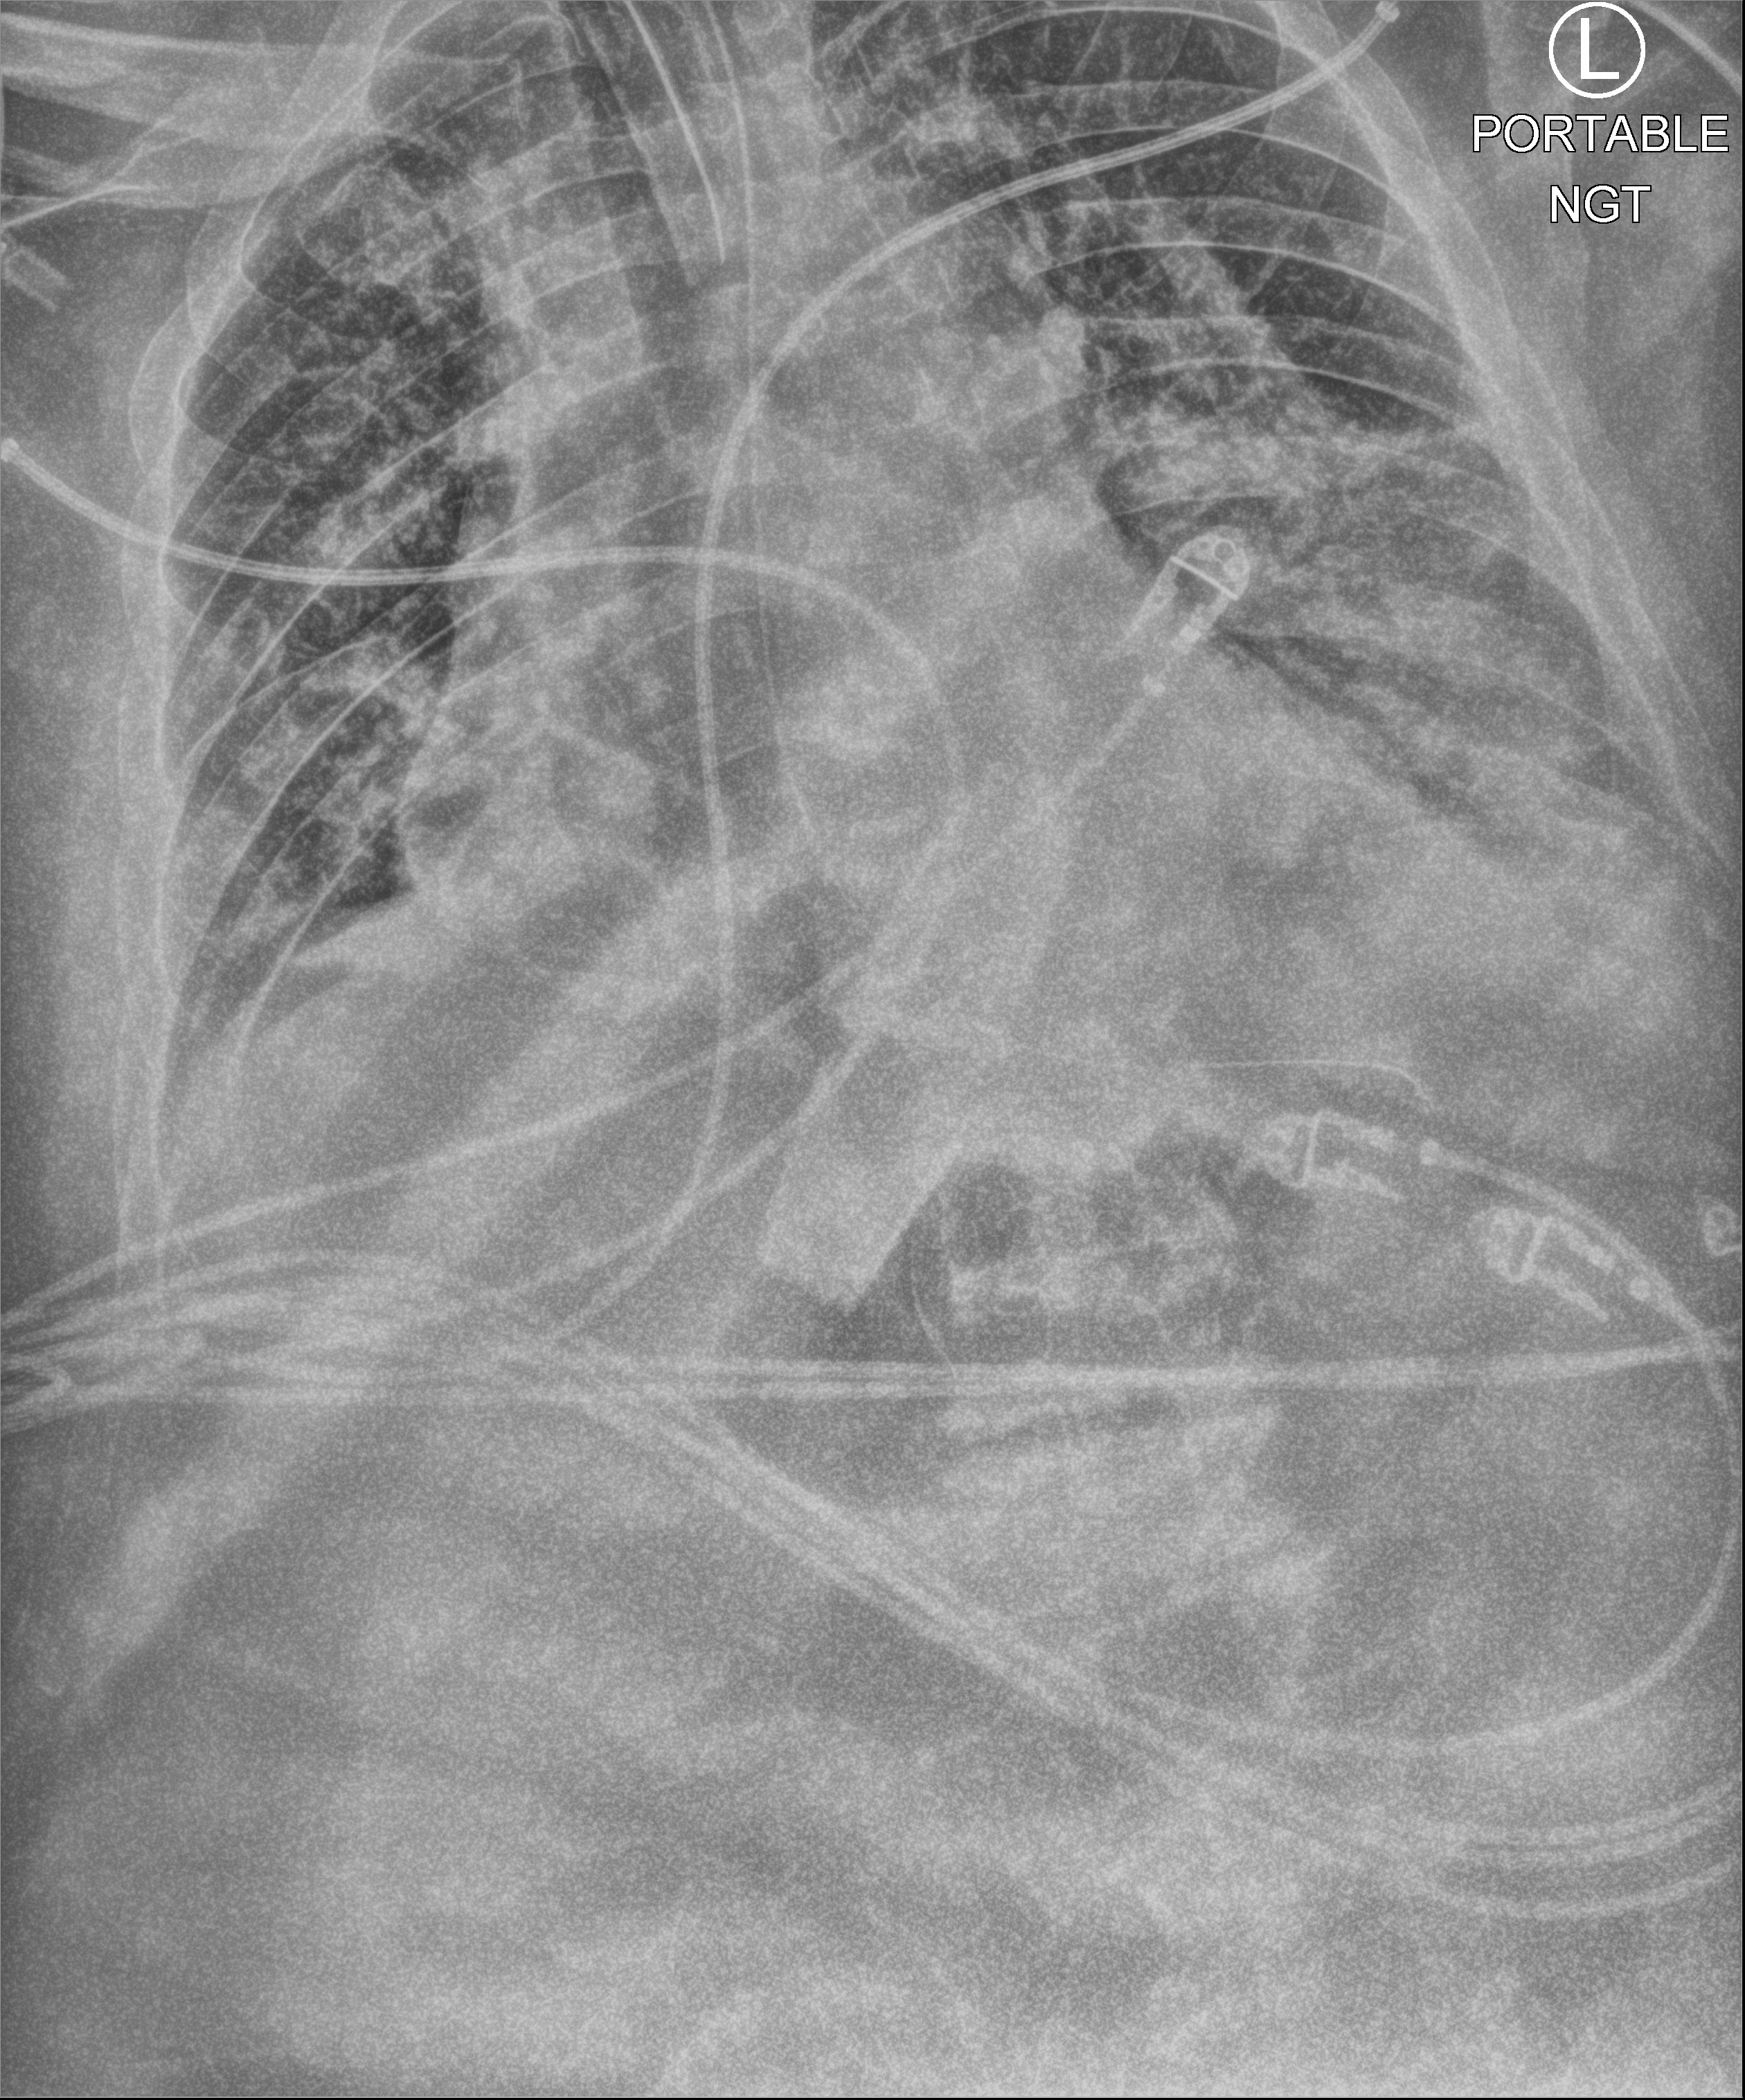
Bedside chest radiograph (computed radiography); anteroposterior (AP) projection. Male patient hospitalised with COVID-19, age 60–74 years.
Hospital-stay facts (about this admission, not read from this image; timing relative to this image not recorded):
- mechanically ventilated during this hospital stay: yes
- admitted to intensive care during this hospital stay: yes
- length of hospital stay: 10 days